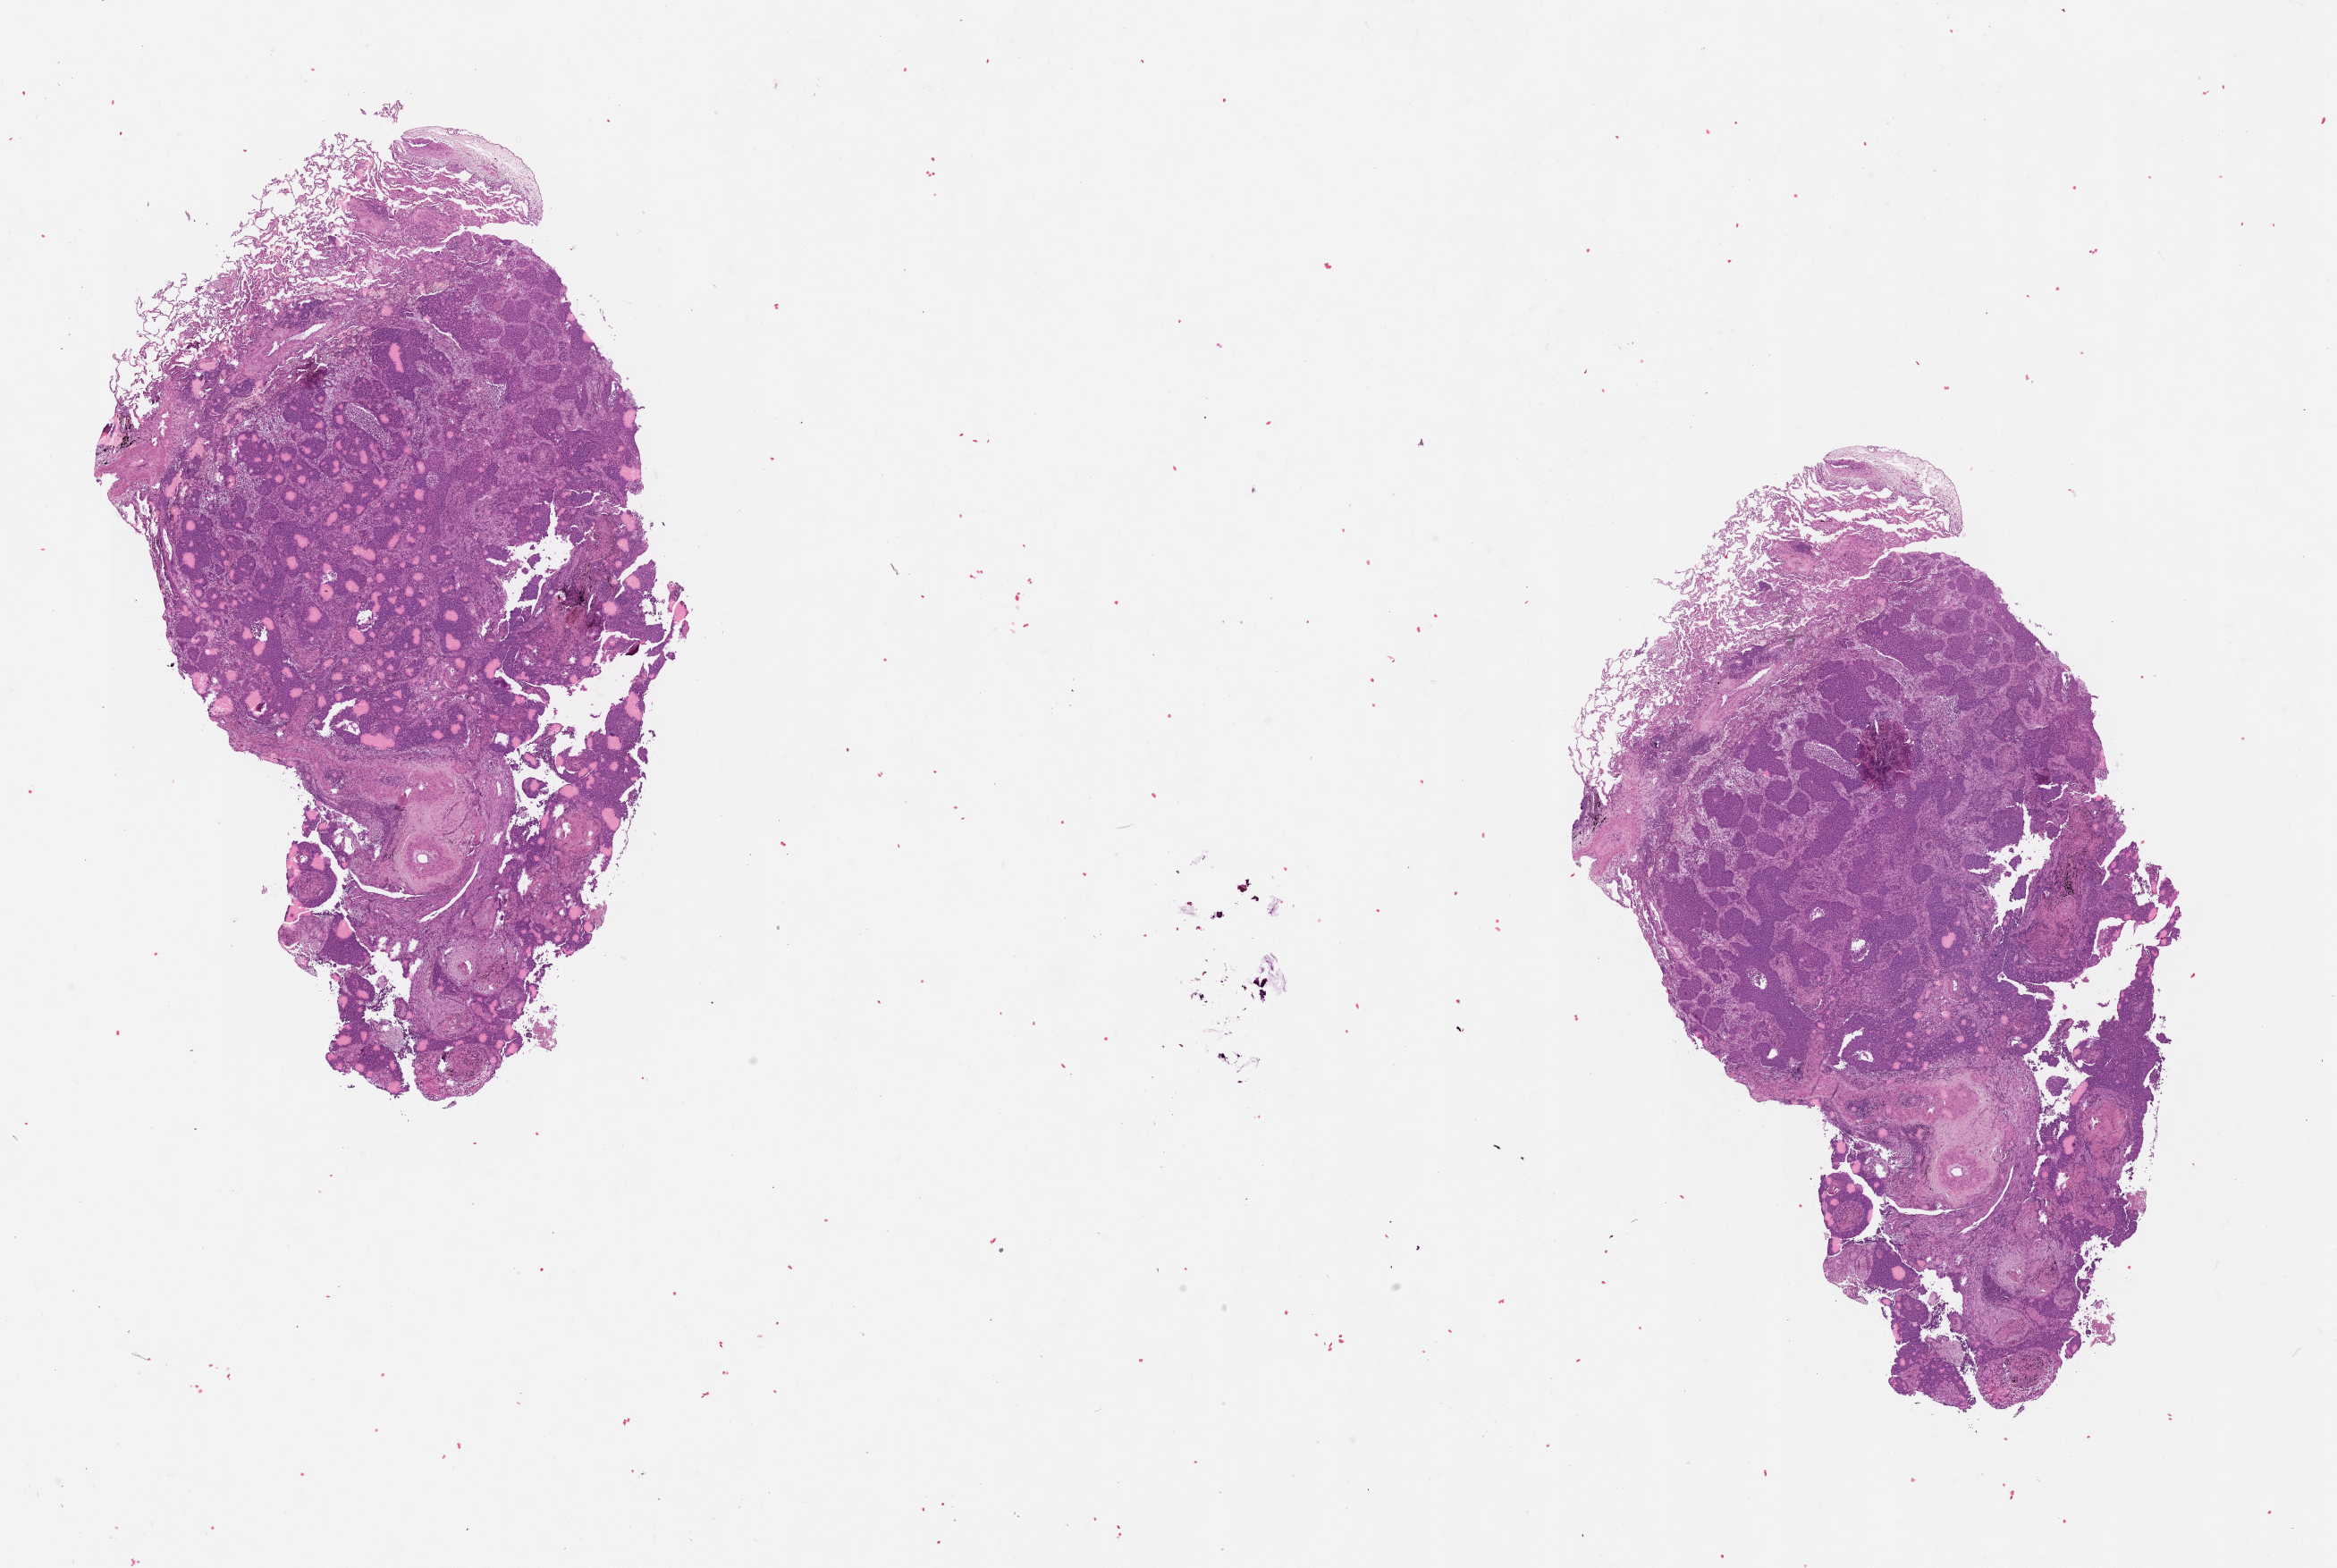
Digitized Hematoxylin and eosin (H&E) stained tissue section (whole slide), a low-resolution overview of the entire scanned area, about 21.0 x 14.1 mm (from a 20x scan); tumour tissue sample, lung. 77-year-old male patient.
Patient diagnosis (cohort enrolment): squamous cell carcinoma (lung).